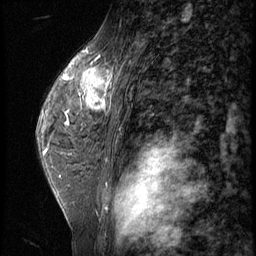
Breast MRI (dynamic contrast-enhanced), one sagittal slice. Slice 40 of 62 in the series (ordered by position). 3 images stored at this slice position (order not interpretable as contrast timing). 1.5 T. TE 4.2 ms, TR 9 ms. 256 × 256 image matrix, field of view 180 × 180 mm. Patient: female, 44 years. From the clinical record (not read from this slice): setting: breast cancer imaged before/during neoadjuvant chemotherapy; receptor status: triple-negative.
Structures marked on this image (semi-automatic segmentation, software-assisted and operator-edited):
- analysis volume of interest (the breast-tissue region the enhancement analysis was run in; not a lesion): bounding box [x1, y1, x2, y2] px = [72, 64, 116, 125]
- tumour enhancement mask (voxels above the 140 % enhancement threshold inside the analysis volume of interest): [80, 64, 115, 114]